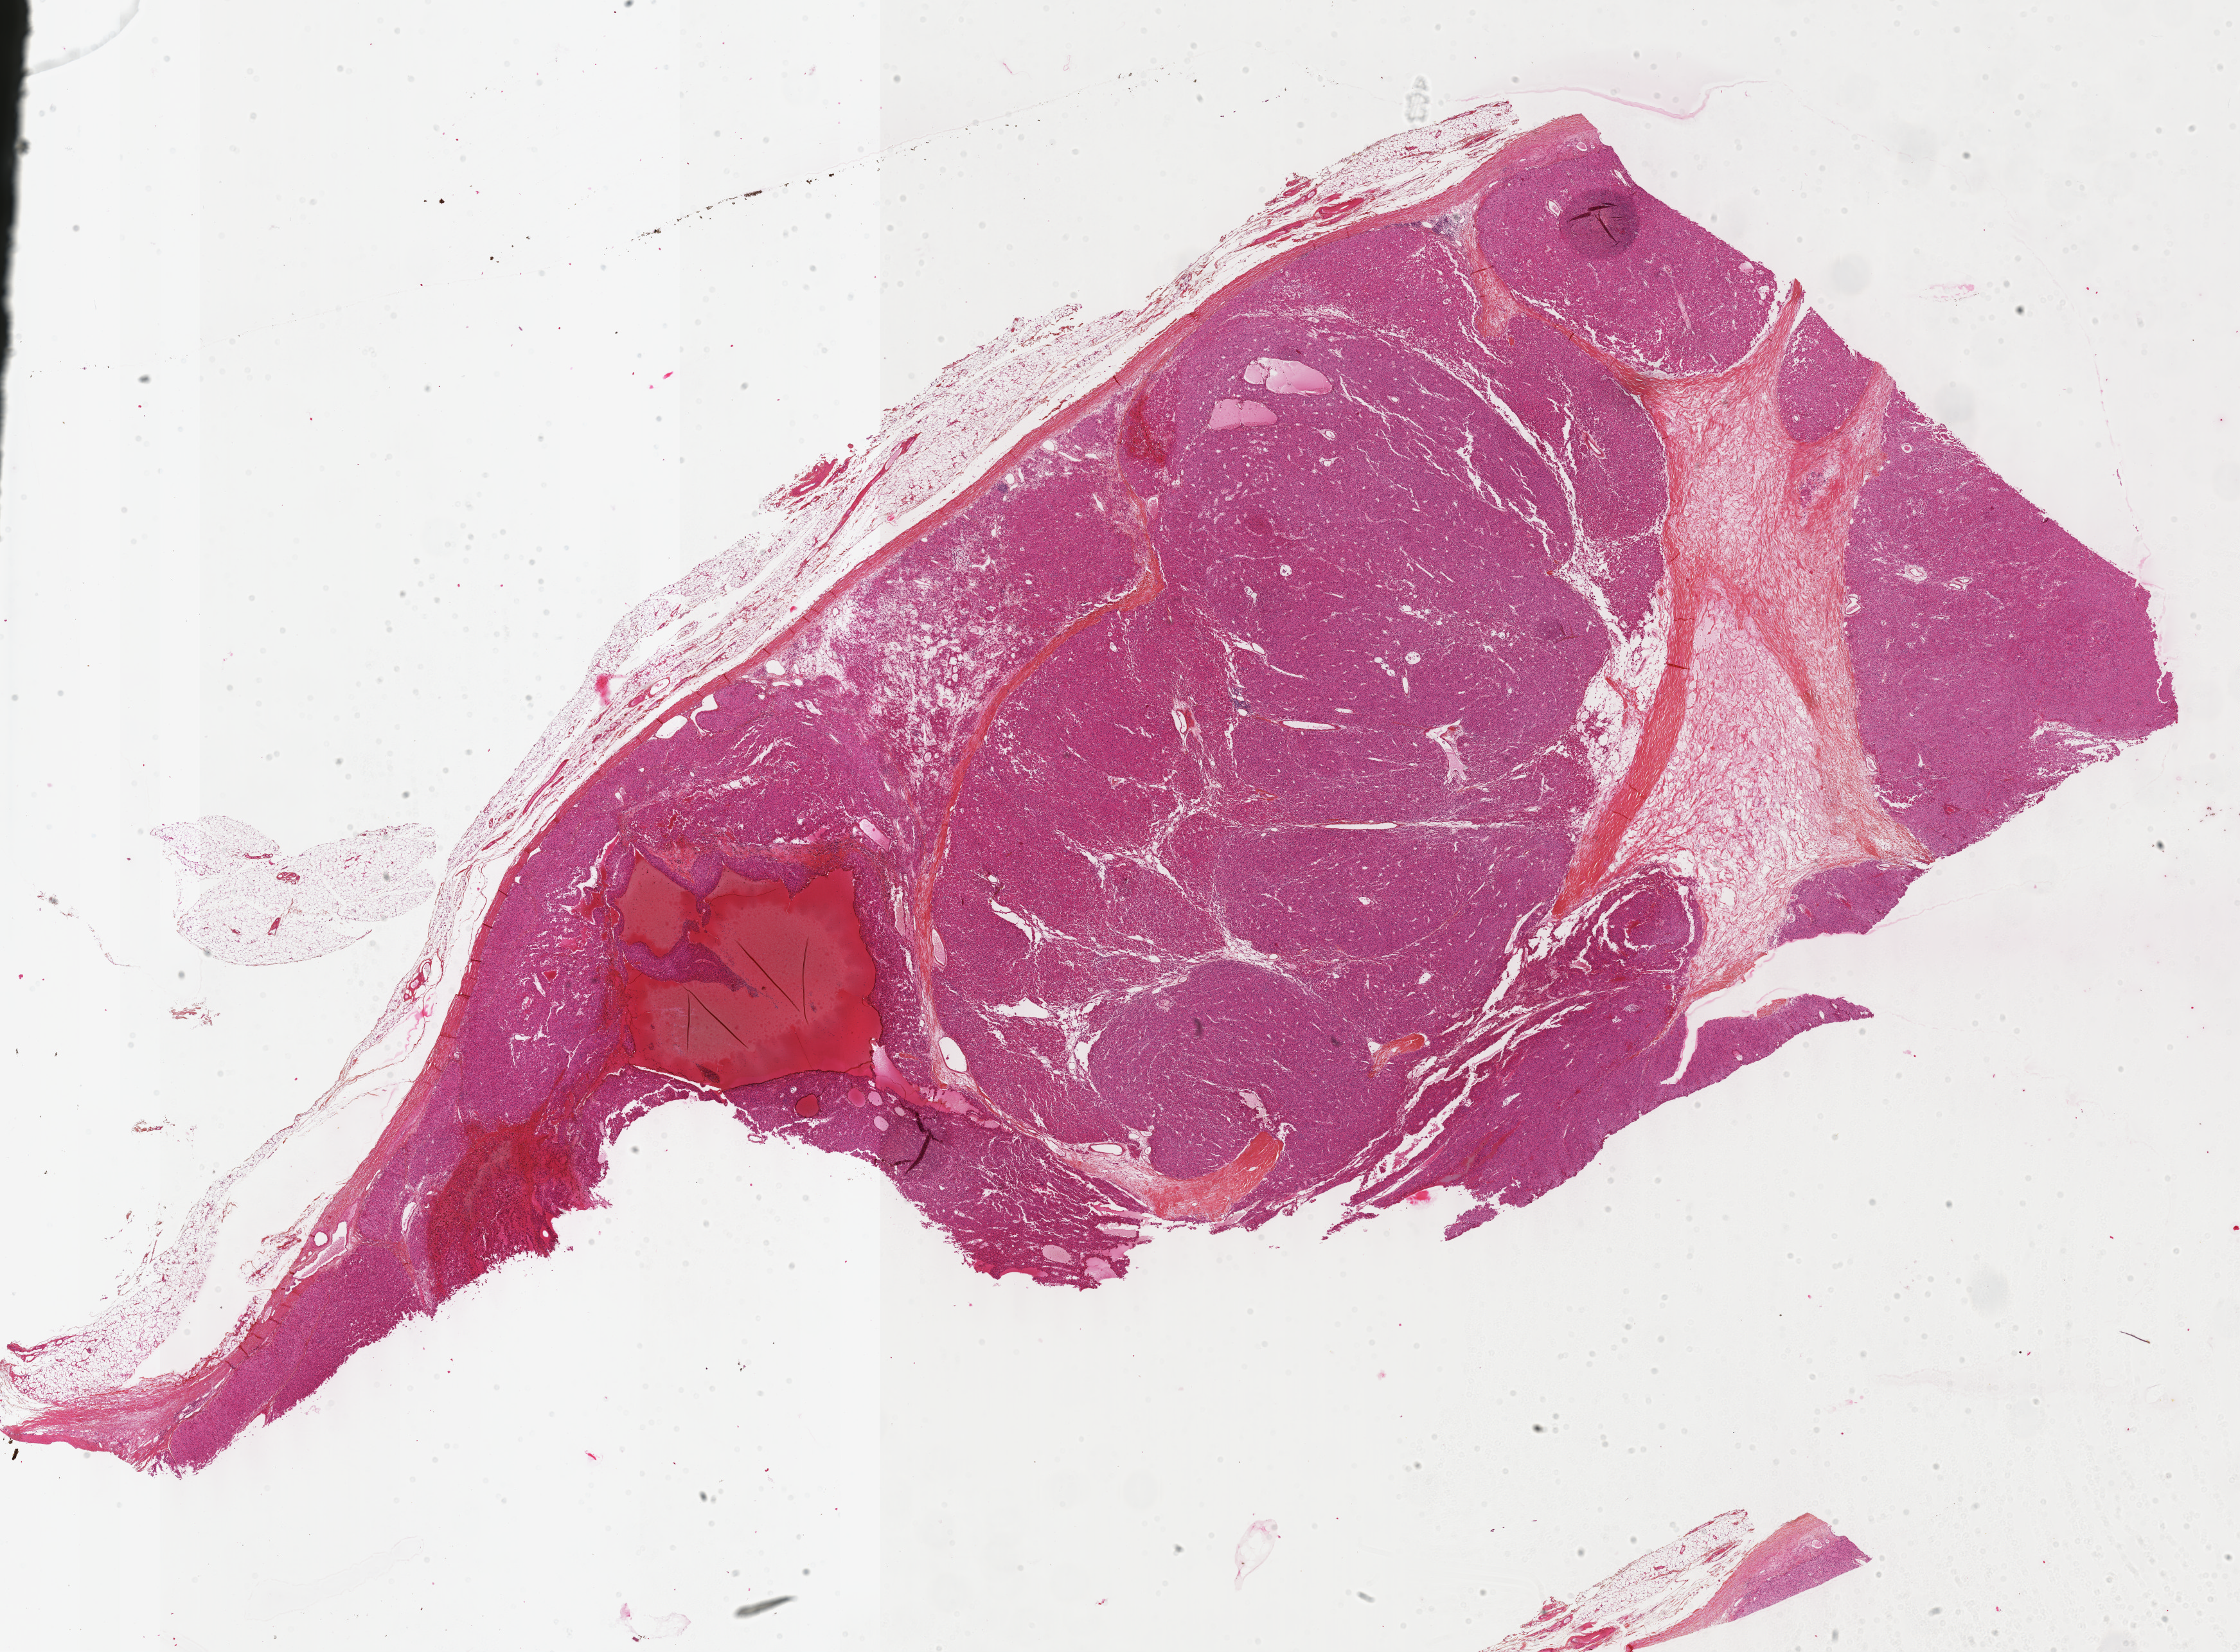
H&E-stained whole-slide image, low-resolution overview of the scanned area, about 28.2 x 20.8 mm (acquisition: 40x scan), formalin-fixed paraffin-embedded (FFPE) diagnostic section, adrenal cortex, primary tumour sample. Male, age 62 years at initial diagnosis.
Diagnosis: Adrenal cortical carcinoma (cortex of adrenal gland).